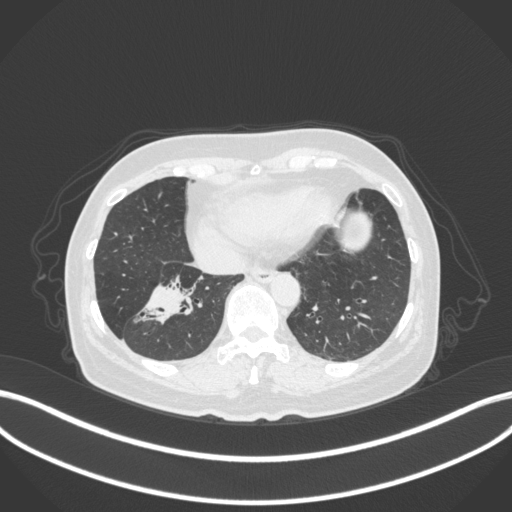
Chest CT, one axial slice; slice 116 of 429 in the series (ordered by position); reconstruction kernel B31f; 120 kVp; lung window (W 1500 / L -600 HU); 1 mm slice thickness; 512 × 512 image matrix, field of view 400 × 400 mm. Patient: female, 67 years. Case-level facts recorded for this patient, not image findings: clinical TNM (as recorded): T1c N1 M0.
Structures marked on this image (bounding box drawn by a radiologist):
- lung tumour (recorded histology: adenocarcinoma): bounding box <127,275,206,330> (left, top, right, bottom; pixels)